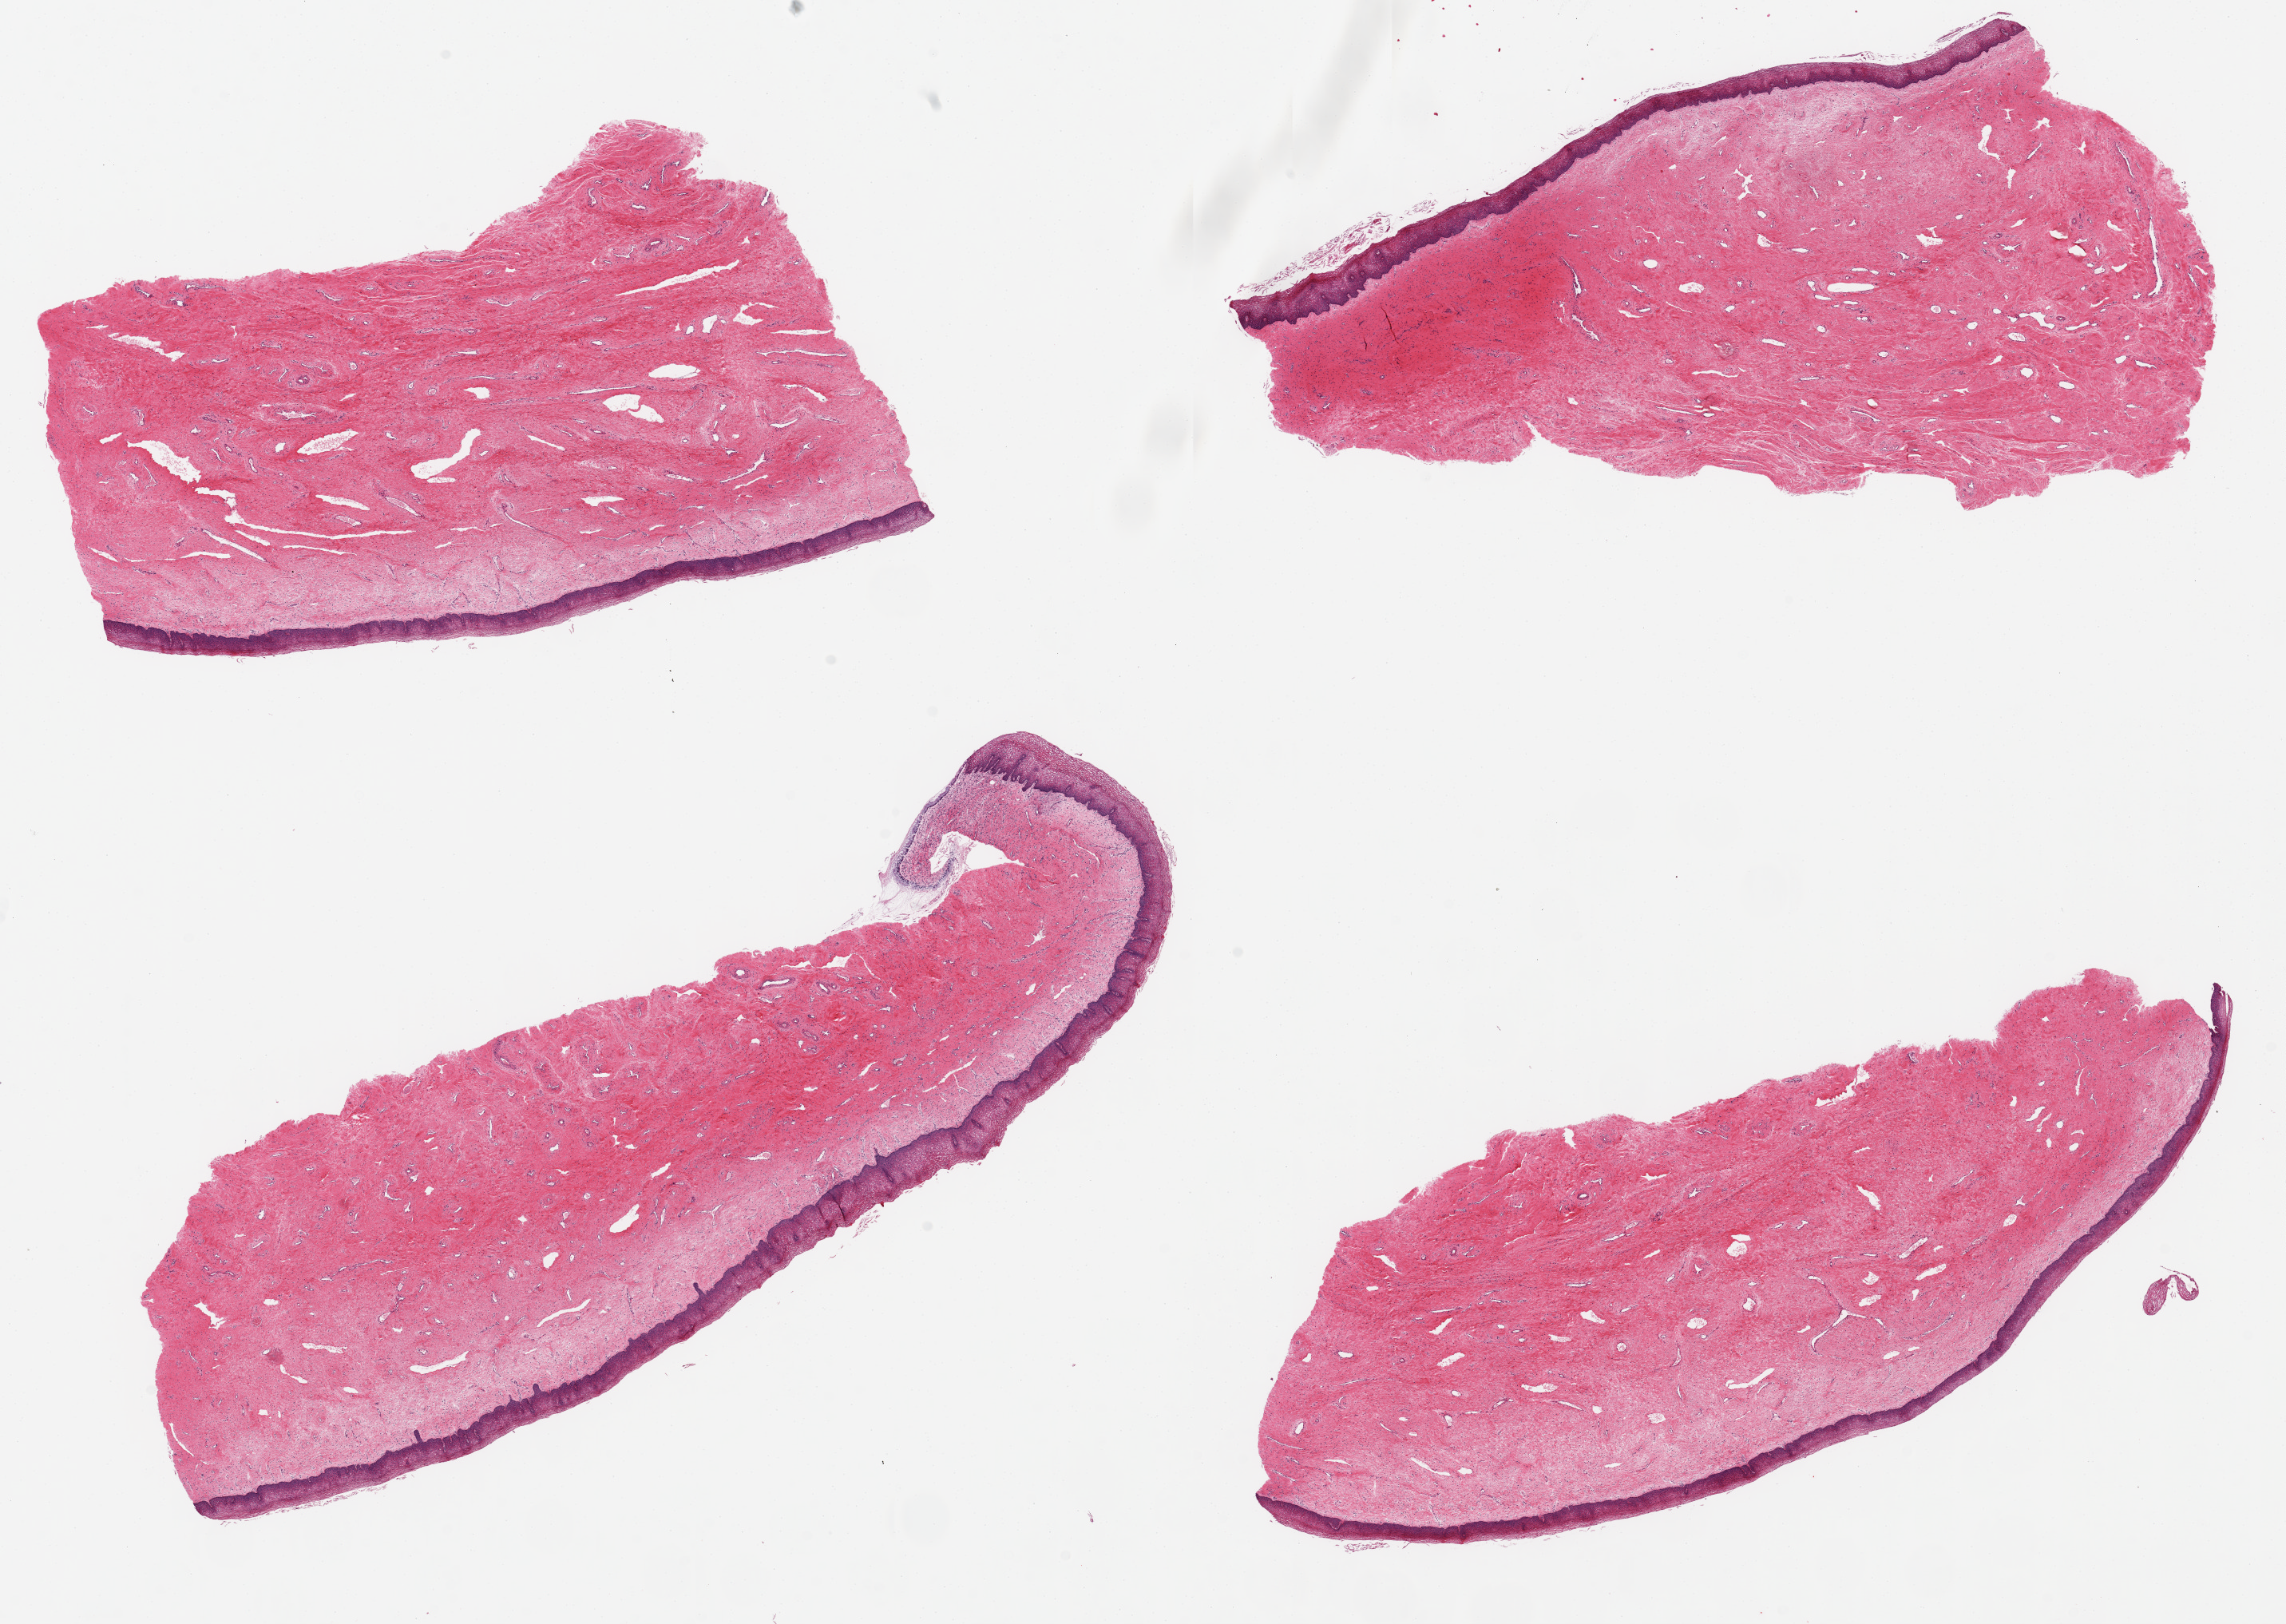
H&E whole-slide image — whole scanned area (about 22.6 x 16.1 mm, slide scanned at 20x) shown as a low-resolution overview; PAXgene-fixed paraffin-embedded (PFPE) section; section of exocervix (target tissue); donor tissue sample. Donor sex: female.
Pathologist's review note for this sample: 4 pieces up to 11.5x4mm, all with good squamous surface up to 0.4 mm thick.